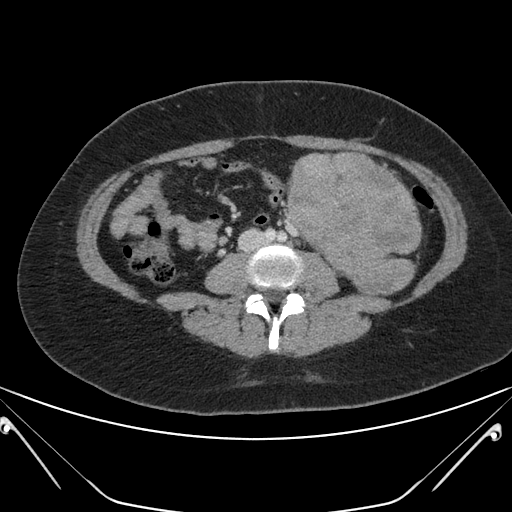
Contrast-enhanced abdominal CT, one axial slice. Position 84 of 168 along the scan axis. 120 kVp. Intravenous contrast given. Soft-tissue window (W 400 / L 40 HU). 3 mm slice thickness. 512 × 512 image matrix, field of view 394 × 394 mm. Patient: female, 26 years. From the clinical record (not read from this slice): diagnosis: adrenocortical carcinoma; tumour side: left adrenal; tumour size at pathology: 28 cm; Ki-67 index: 20 %; stage (as recorded): 2.
Structures marked on this image (semi-automatic segmentation, software-assisted and operator-edited):
- mass: bounding box (x1, y1, x2, y2) in pixels: (284, 151, 421, 294)